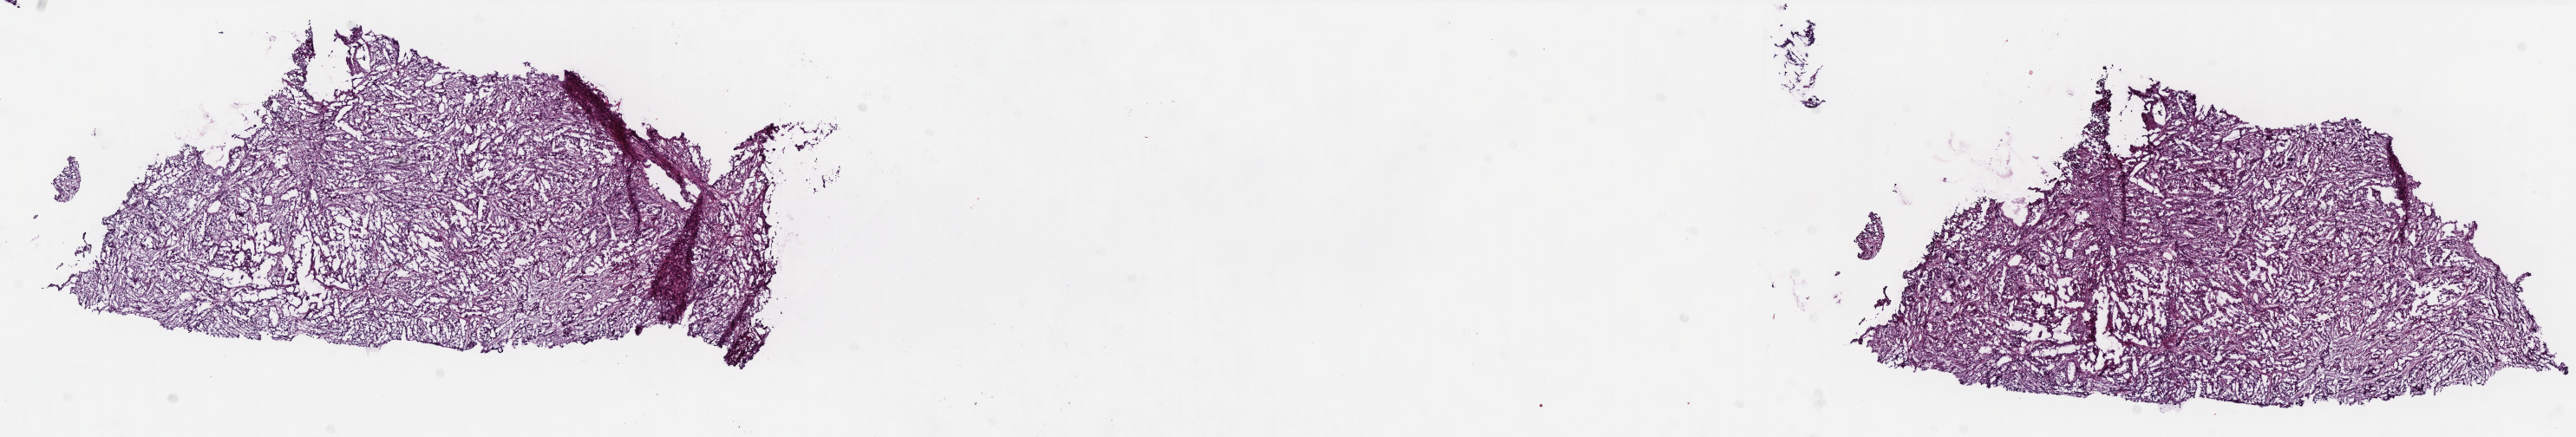
Digitized H&E-stained tissue section (whole slide), shown as a low-resolution overview of the whole scanned area (about 23.8 x 4.0 mm, slide scanned at 40x), frozen section, sample: primary tumour, uterus. Patient: female, age at initial diagnosis 64 years. Histologic grade: G3 (poorly differentiated). Composition of this section per pathologist review: tumour cells 54%, tumour nuclei 60%, normal cells 0%, stromal cells 40%, necrosis 6%. Inflammatory infiltration, as recorded: lymphocyte infiltration 14%, monocyte infiltration 0%, neutrophil infiltration 0%.
FIGO stage: II. Histologic diagnosis: Endometrioid adenocarcinoma, NOS. Lymph nodes positive (case pathology): 0 of 20 examined.